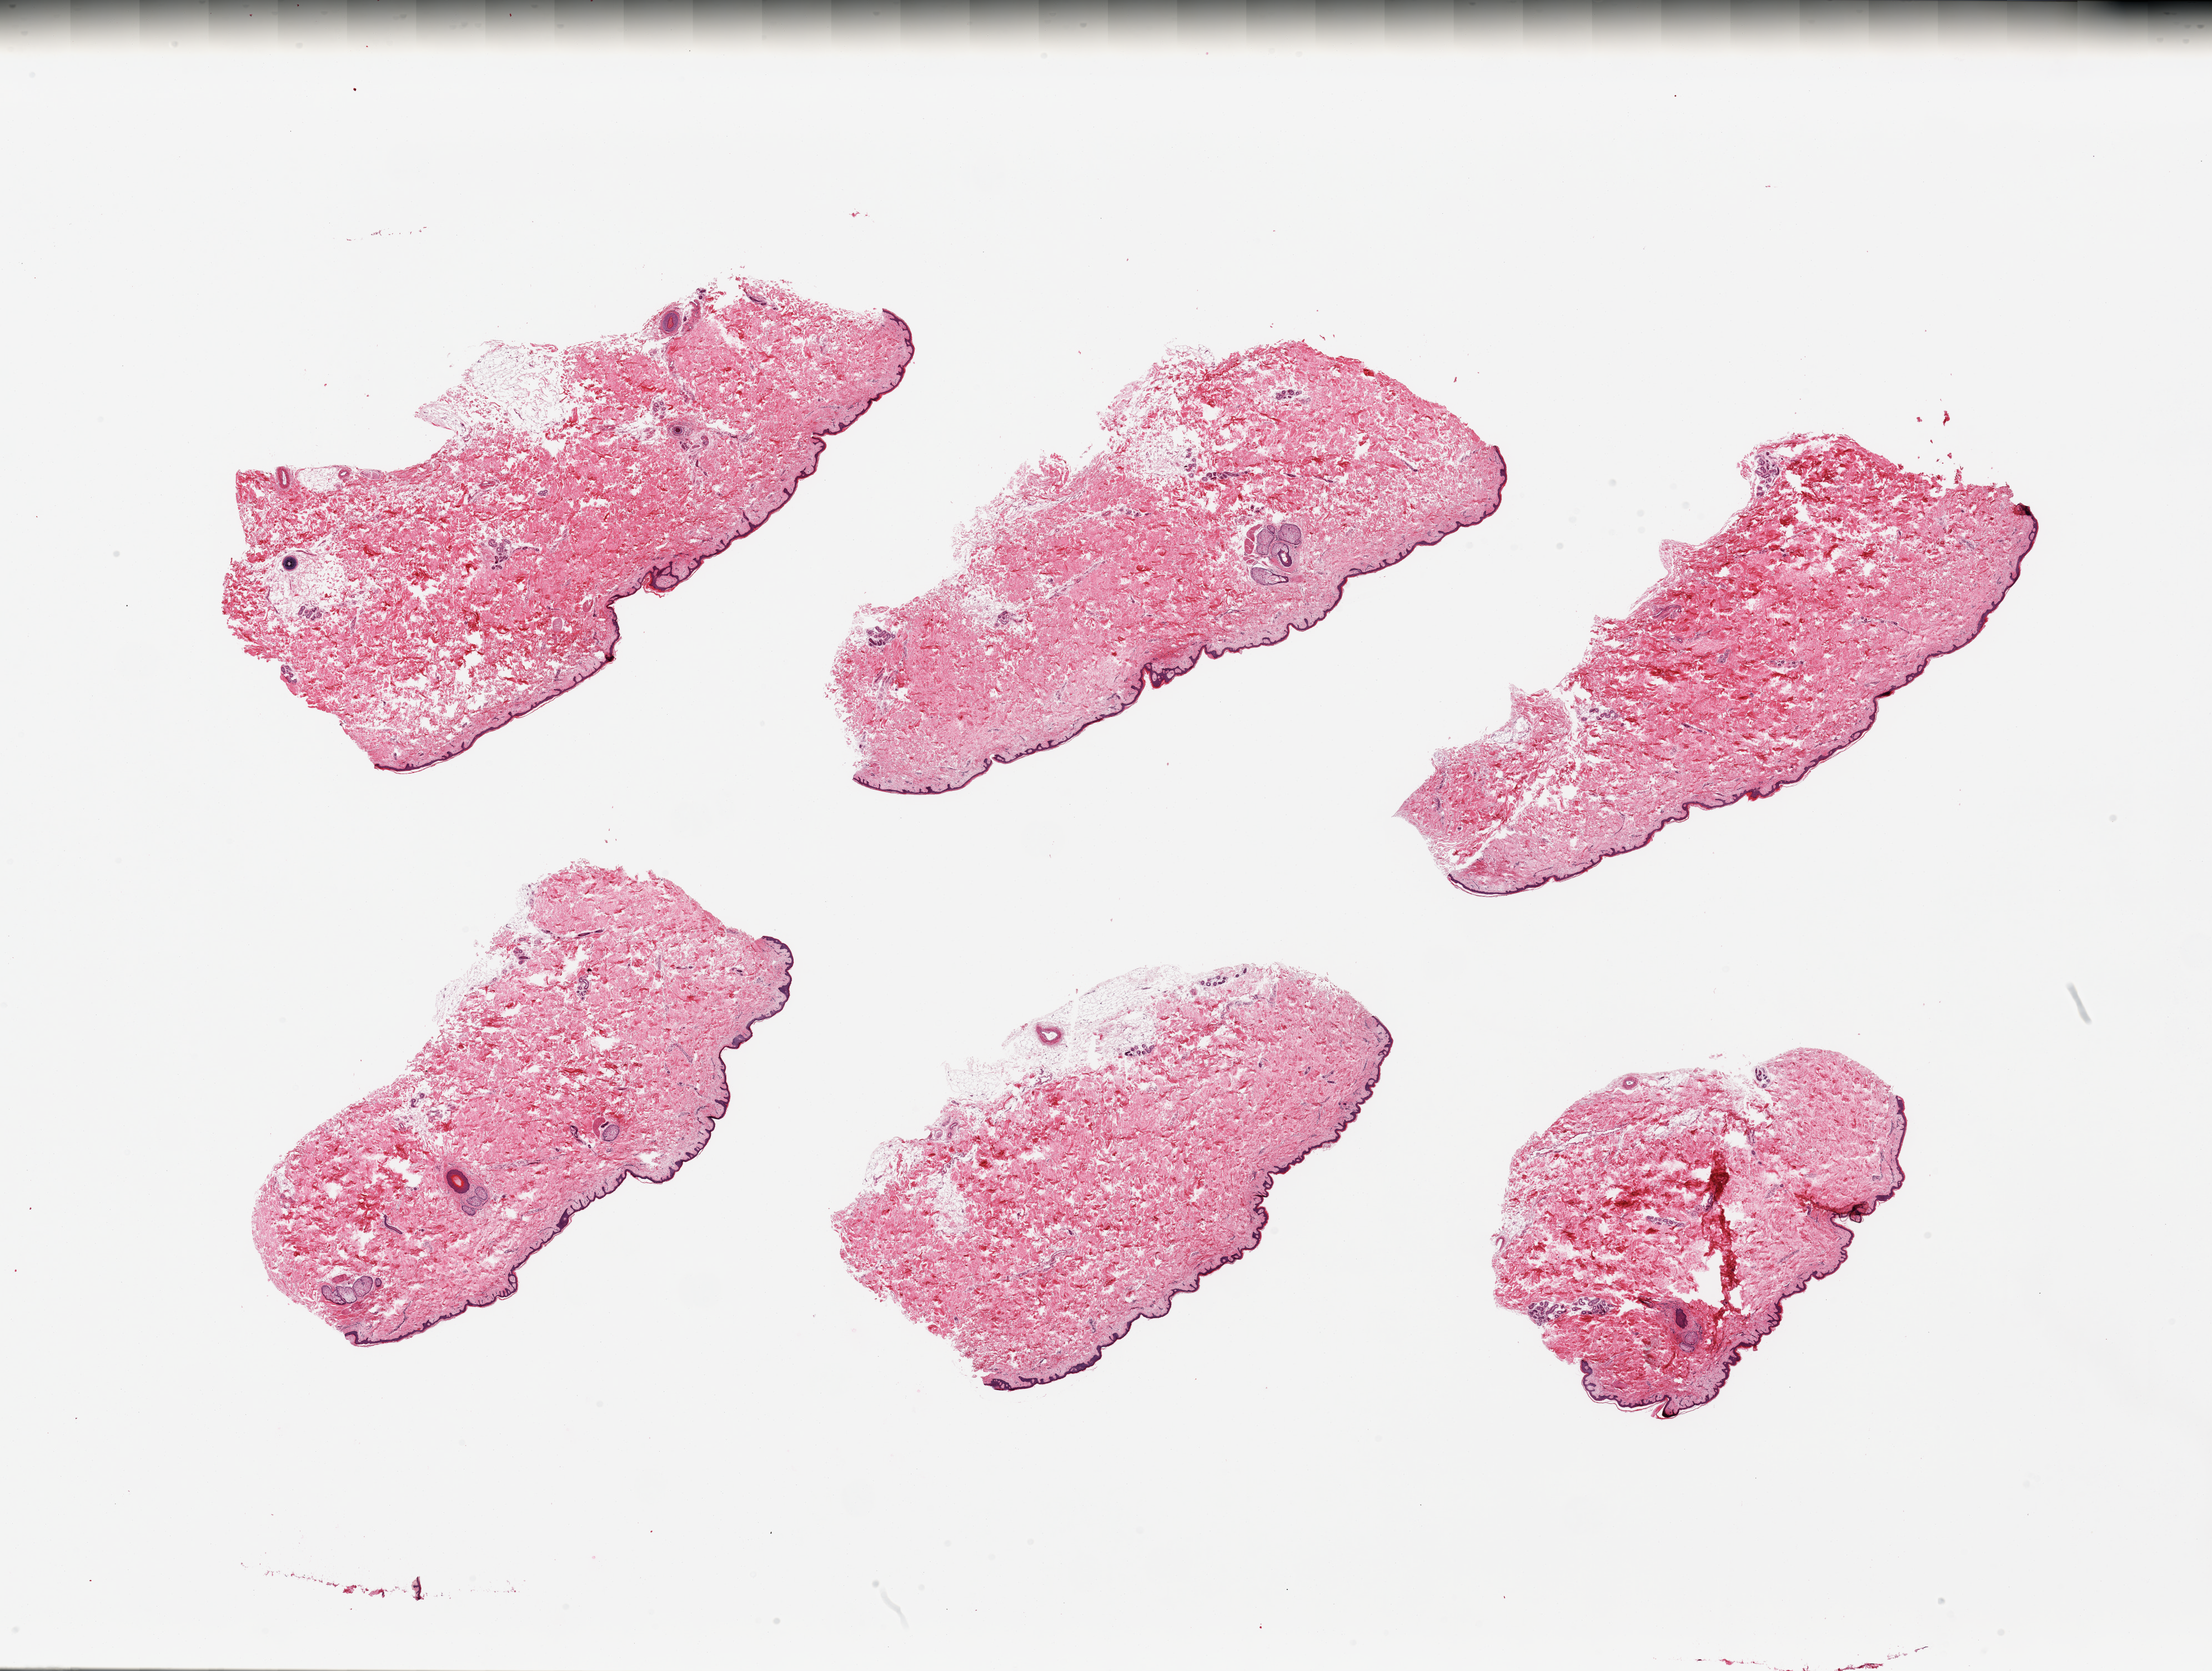
Digitized hematoxylin and eosin (H&E)-stained section, brightfield, whole scanned area (about 31.5 x 23.8 mm, from a 20x scan) shown as a low-resolution overview; PAXgene-fixed, paraffin-embedded tissue; sampled site (target tissue): skin of suprapubic region; donor tissue sample. Donor: male.
Pathologist's review note for this sample: 6 pieces; 5-10% residual attached fat.